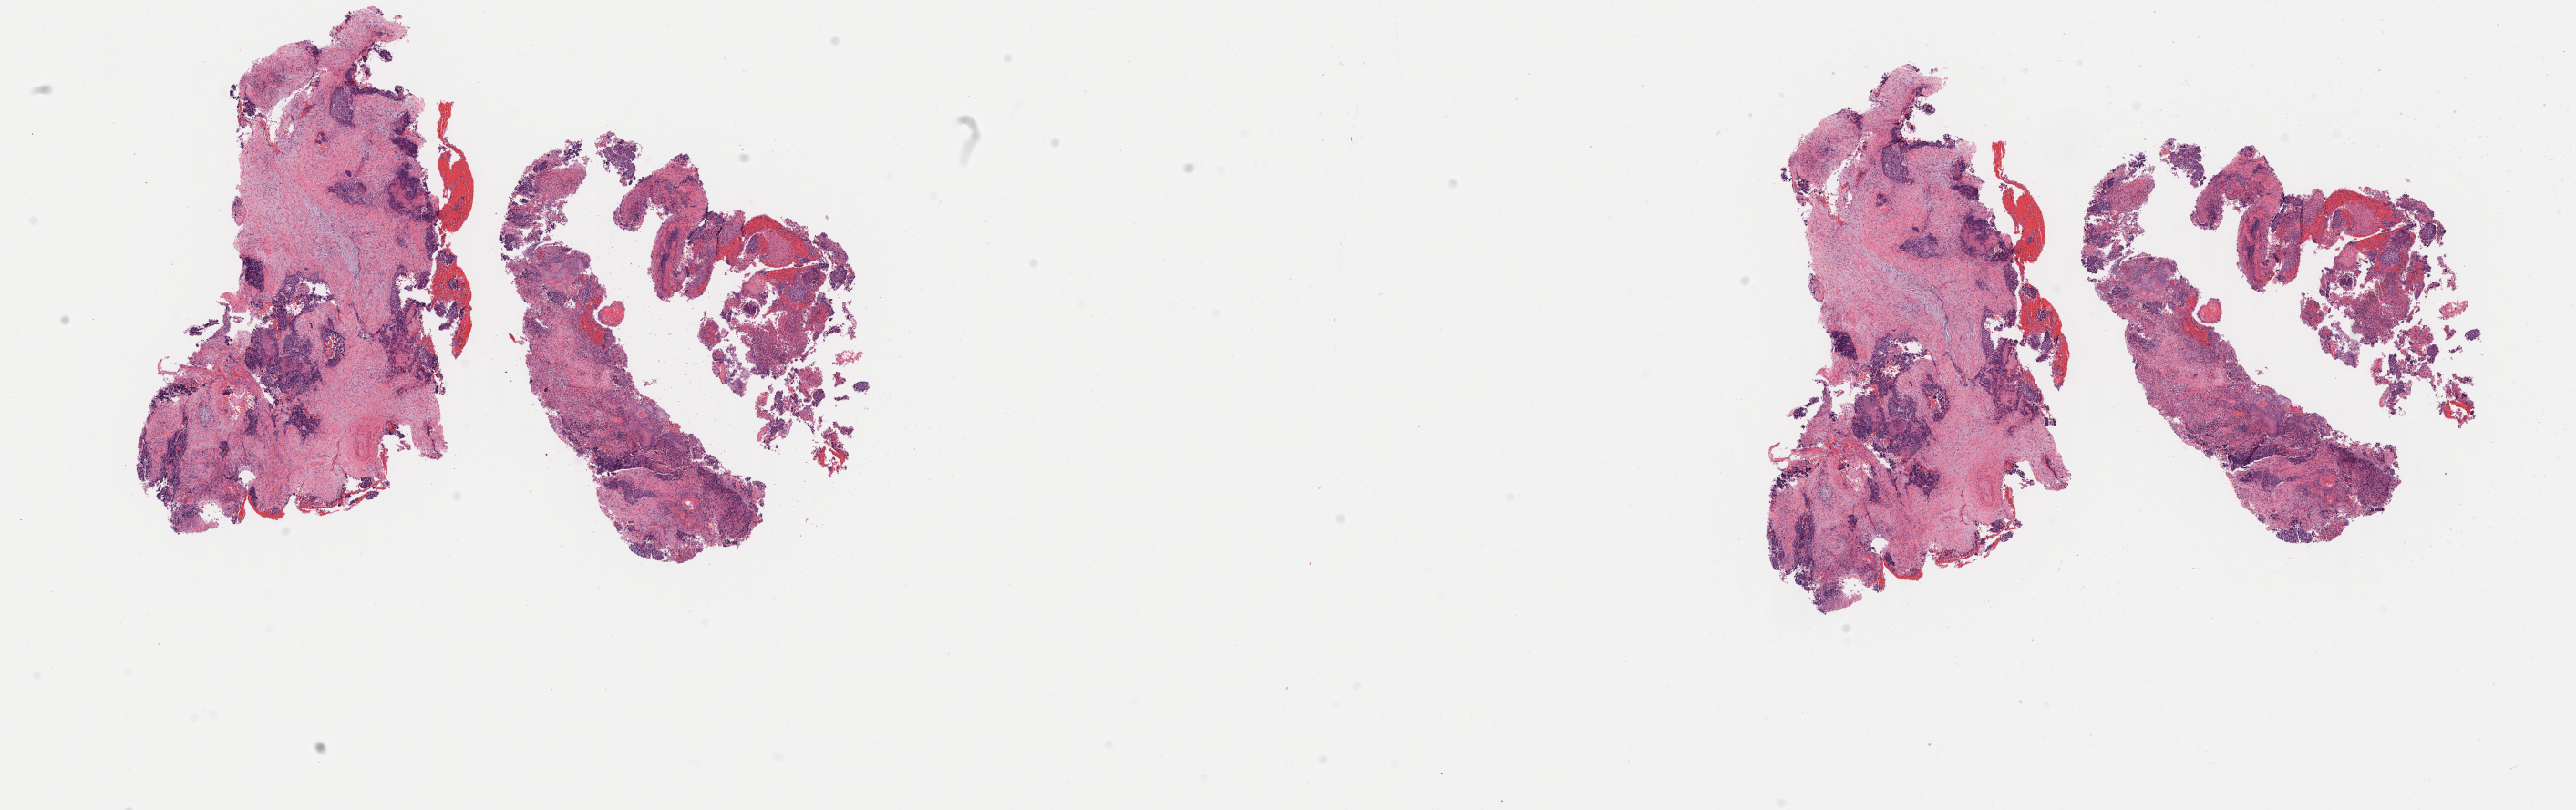
Whole-slide image, hematoxylin and eosin (H&E) stain, shown as a low-resolution overview of the whole scanned area (about 22.5 x 7.1 mm). Specimen: tumor tissue. Anatomic site: cervix. Female patient, aged 47.
Diagnosis: Squamous cell carcinoma, large cell, nonkeratinizing, NOS.